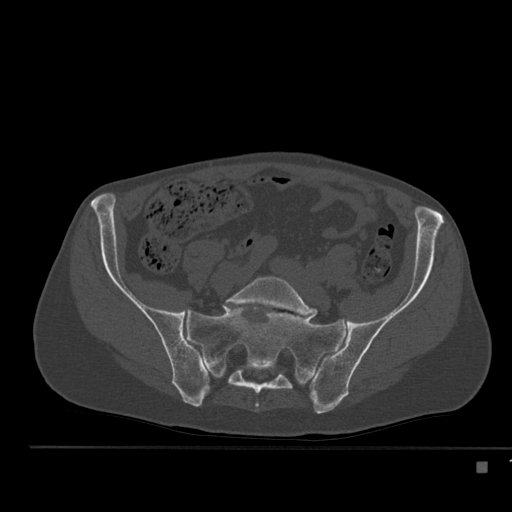
CT including the spine, one axial slice. Slice 107 of 517 in the series (ordered by position). Reconstruction kernel Br40s. Bone window (W 1800 / L 400 HU). 512 × 512 image matrix, field of view 408 × 408 mm. Male patient, age 70 years. Case-level facts recorded for this patient, not image findings: primary cancer: renal.
Annotated regions visible in this slice (semi-automatic segmentation, software-assisted and operator-edited):
- L5 vertebra: bounding box (x1, y1, x2, y2) in pixels: (225, 276, 317, 316)